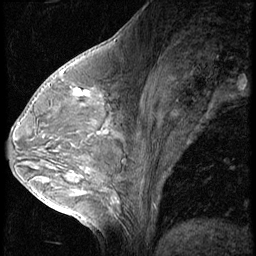
Breast MRI (dynamic contrast-enhanced), one sagittal slice. Position 30 of 56 along the scan axis. 3 images stored at this slice position (order not interpretable as contrast timing). 1.5 T. TE 4.2 ms, TR 9 ms. 2.5 mm slice thickness. 256 × 256 image matrix. Female patient, age 54 years. From the clinical record (not read from this slice): setting: breast cancer imaged before/during neoadjuvant chemotherapy; receptor status: triple-negative.
Annotated regions visible in this slice (semi-automatic segmentation, software-assisted and operator-edited):
- analysis volume of interest (the breast-tissue region the enhancement analysis was run in; not a lesion): bounding box (x1, y1, x2, y2) in pixels: (62, 80, 115, 128)
- tumour enhancement mask (voxels above the 140 % enhancement threshold inside the analysis volume of interest): (75, 89, 89, 97)